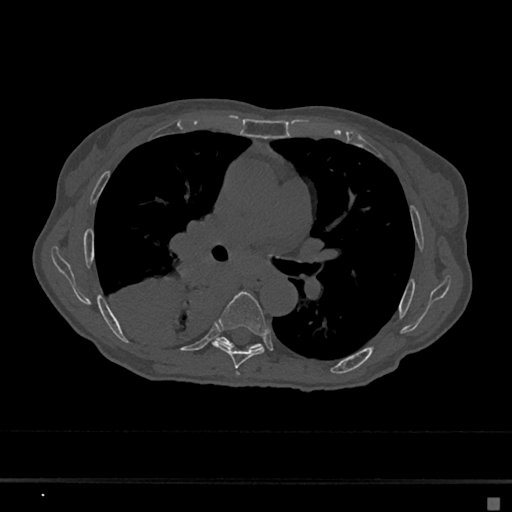
CT including the spine, one axial slice; position 405 of 797 along the scan axis; reconstruction kernel Br40s/3; 120 kVp; bone window (W 1800 / L 400 HU); 0.5 mm slice thickness; 512 × 512 image matrix, field of view 360 × 360 mm. Patient: female, 68 years. Case-level facts recorded for this patient, not image findings: primary cancer: renal.
Annotated regions visible in this slice (semi-automatically segmented with operator editing):
- T5 vertebra: box from (x=236, y=372) to (x=240, y=375) px
- T6 vertebra: (x=213, y=291)–(x=269, y=368)
- T7 vertebra: (x=218, y=337)–(x=262, y=348)